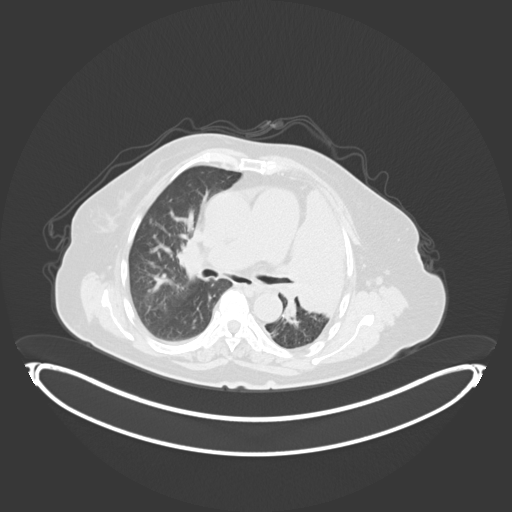
Chest CT, one axial slice; position 204 of 284 along the scan axis; reconstruction kernel B30f; 120 kVp; lung window (W 1500 / L -600 HU); 3 mm slice thickness; 512 × 512 image matrix, field of view 500 × 500 mm. Female patient, age 75 years. From the clinical record (not read from this slice): clinical TNM (as recorded): T3 N3 M1.
Annotated regions visible in this slice (rectangle marked by the reading radiologist):
- lung tumour (recorded histology: adenocarcinoma): bounding box (x1, y1, x2, y2) in pixels: (282, 179, 350, 320)